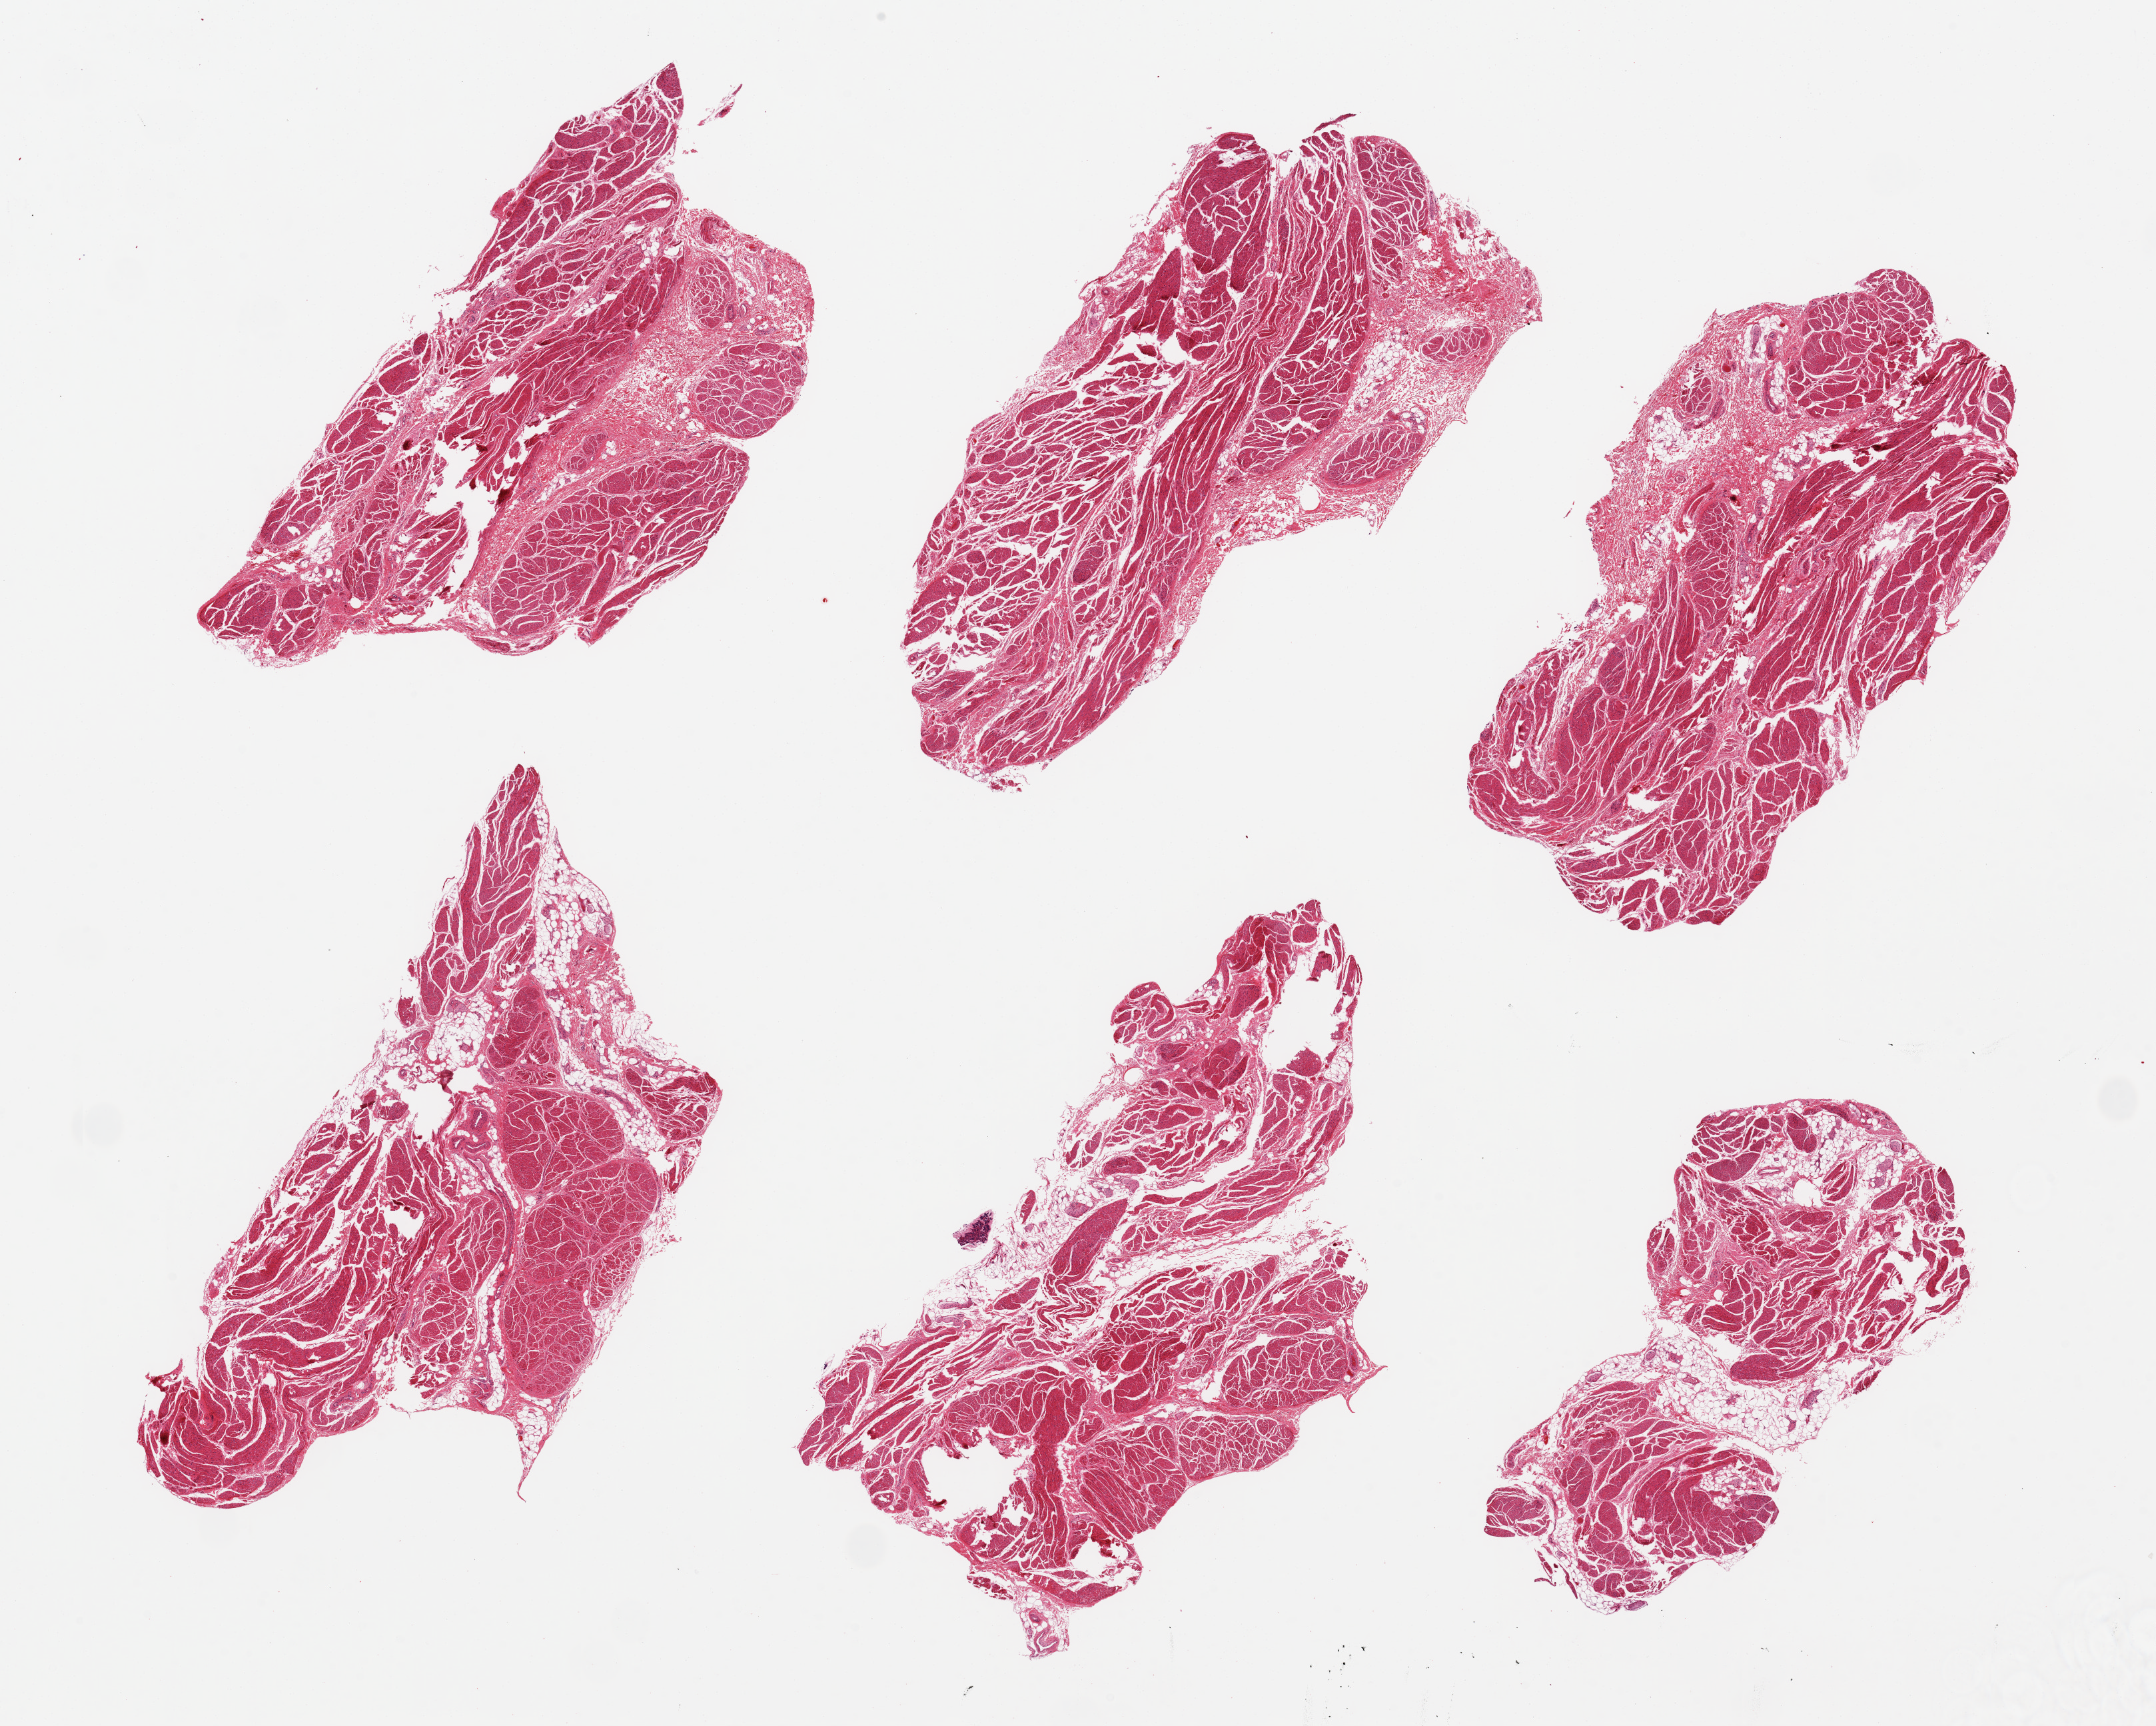
Whole-slide image, hematoxylin and eosin (H&E) stain — shown as a low-resolution overview of the whole scanned area (about 25.6 x 20.5 mm). PAXgene-fixed, paraffin-embedded tissue. Sampled site (target tissue): urinary bladder. Donor tissue sample.
Review note (as recorded): 6 ~8.5x4mm pieces; urothelium completely sloughed/denuded.